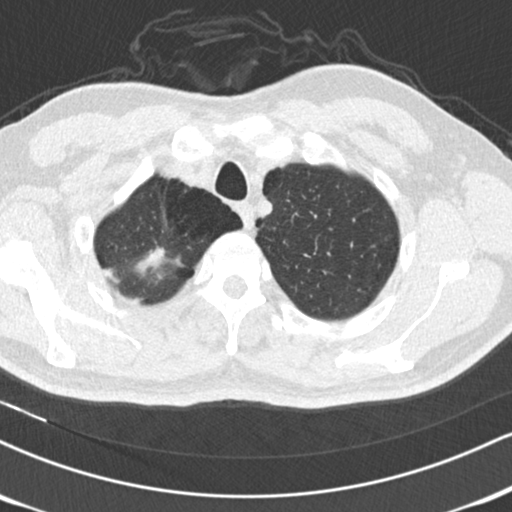
Chest CT (low-dose screening protocol), one axial image, second screening round (one year after baseline), lung window (W 1500 / L -600 HU), 2 mm slice thickness, standard (soft-tissue) reconstruction kernel (B30f), 512 × 512 image matrix, field of view 322 × 322 mm. Male, age 56 years at enrolment.
Expert reader's lesion annotation, bounding box (x1, y1, x2, y2) in pixels: (123, 236, 181, 282). Reader record for this screening exam (exam-level; its link to the box is not recorded): non-calcified nodule or mass ≥4 mm, right upper lobe, 13 × 10 mm, spiculated (stellate) margins, soft tissue attenuation. Official screen result: positive, other. Later outcome: lung cancer diagnosed 384 days after this screen (after the third annual screen) — adenocarcinoma, NOS, right upper lobe, moderately differentiated (G2), stage IA (AJCC 6th edition), 9 mm at pathology.